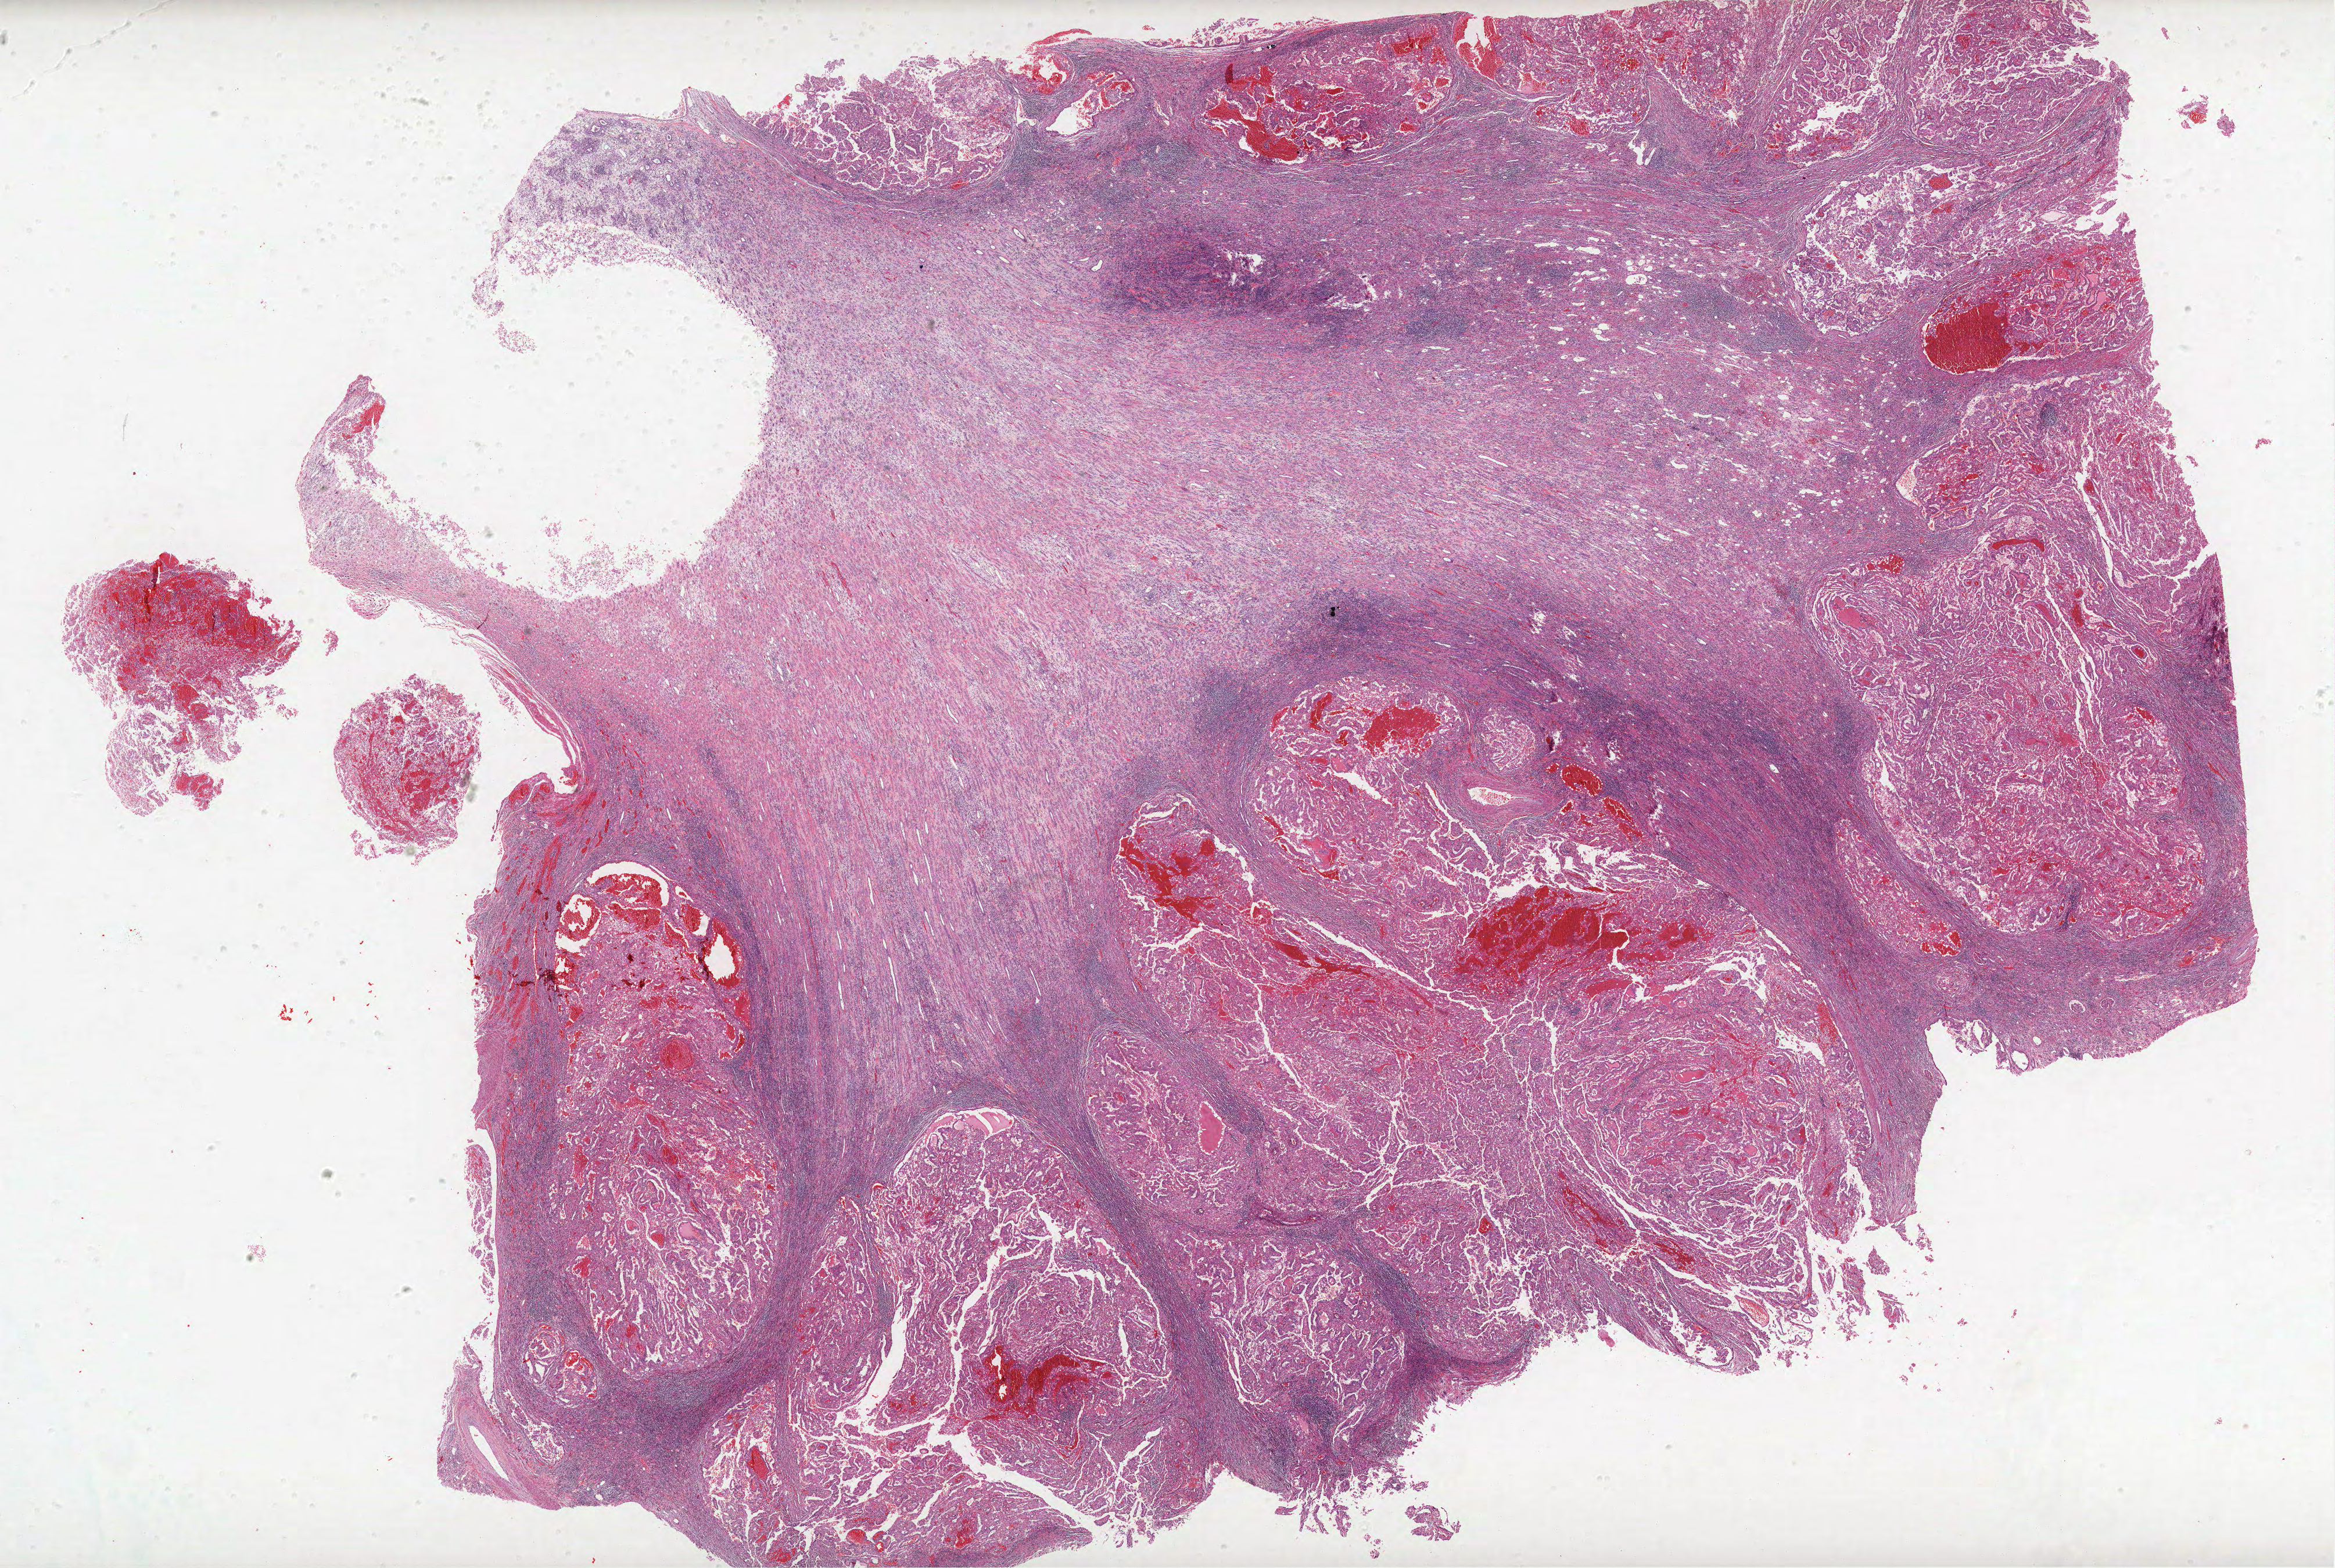
Hematoxylin and eosin (H&E) stained whole-slide image — whole scanned area (about 32.1 x 21.6 mm, from a 40x scan) shown as a low-resolution overview; formalin-fixed paraffin-embedded (FFPE) diagnostic section; sample: primary tumour, kidney. Patient: male, age at initial diagnosis 54 years.
Pathologic diagnosis: Papillary adenocarcinoma, NOS.